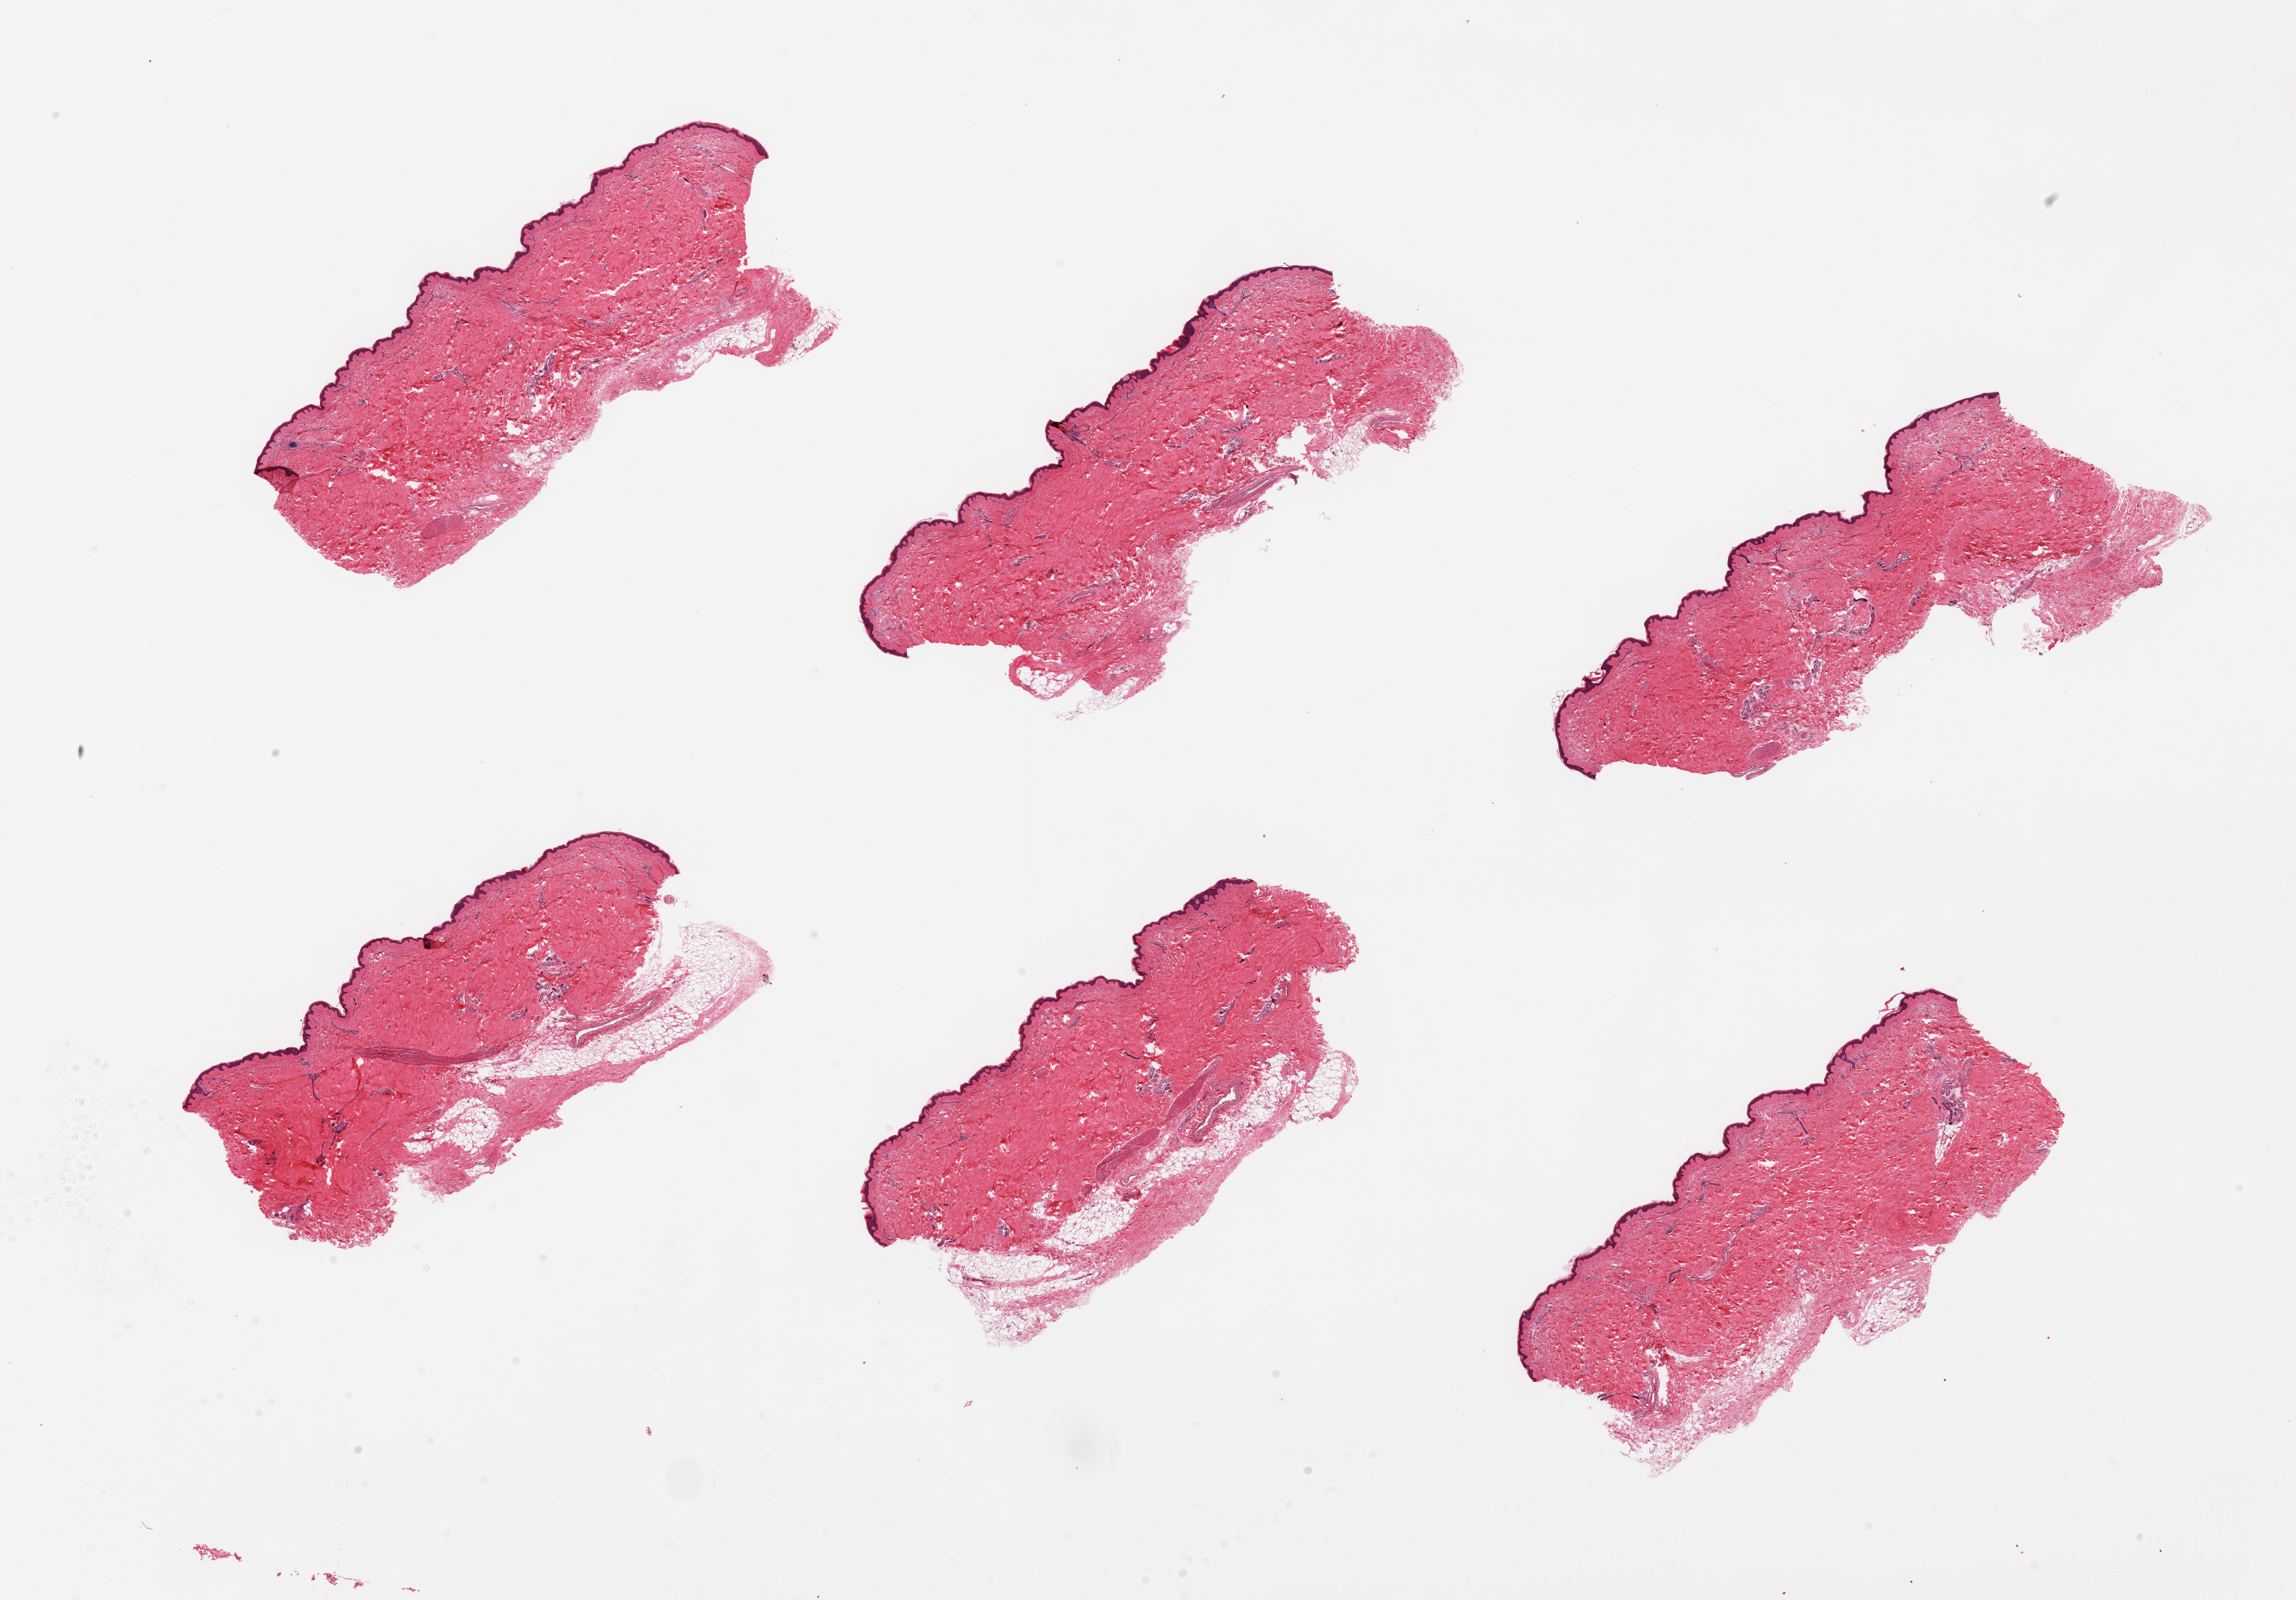
H&E whole-slide image — whole scanned area (about 28.5 x 19.9 mm) shown as a low-resolution overview, PAXgene-fixed paraffin-embedded (PFPE) section, target tissue: skin of lower leg, donor tissue sample. Donor sex: male.
* review note (as recorded): 6 pieces; up to 1 mm subcutaneous fat on 3 of 6; virtually no dermal fat